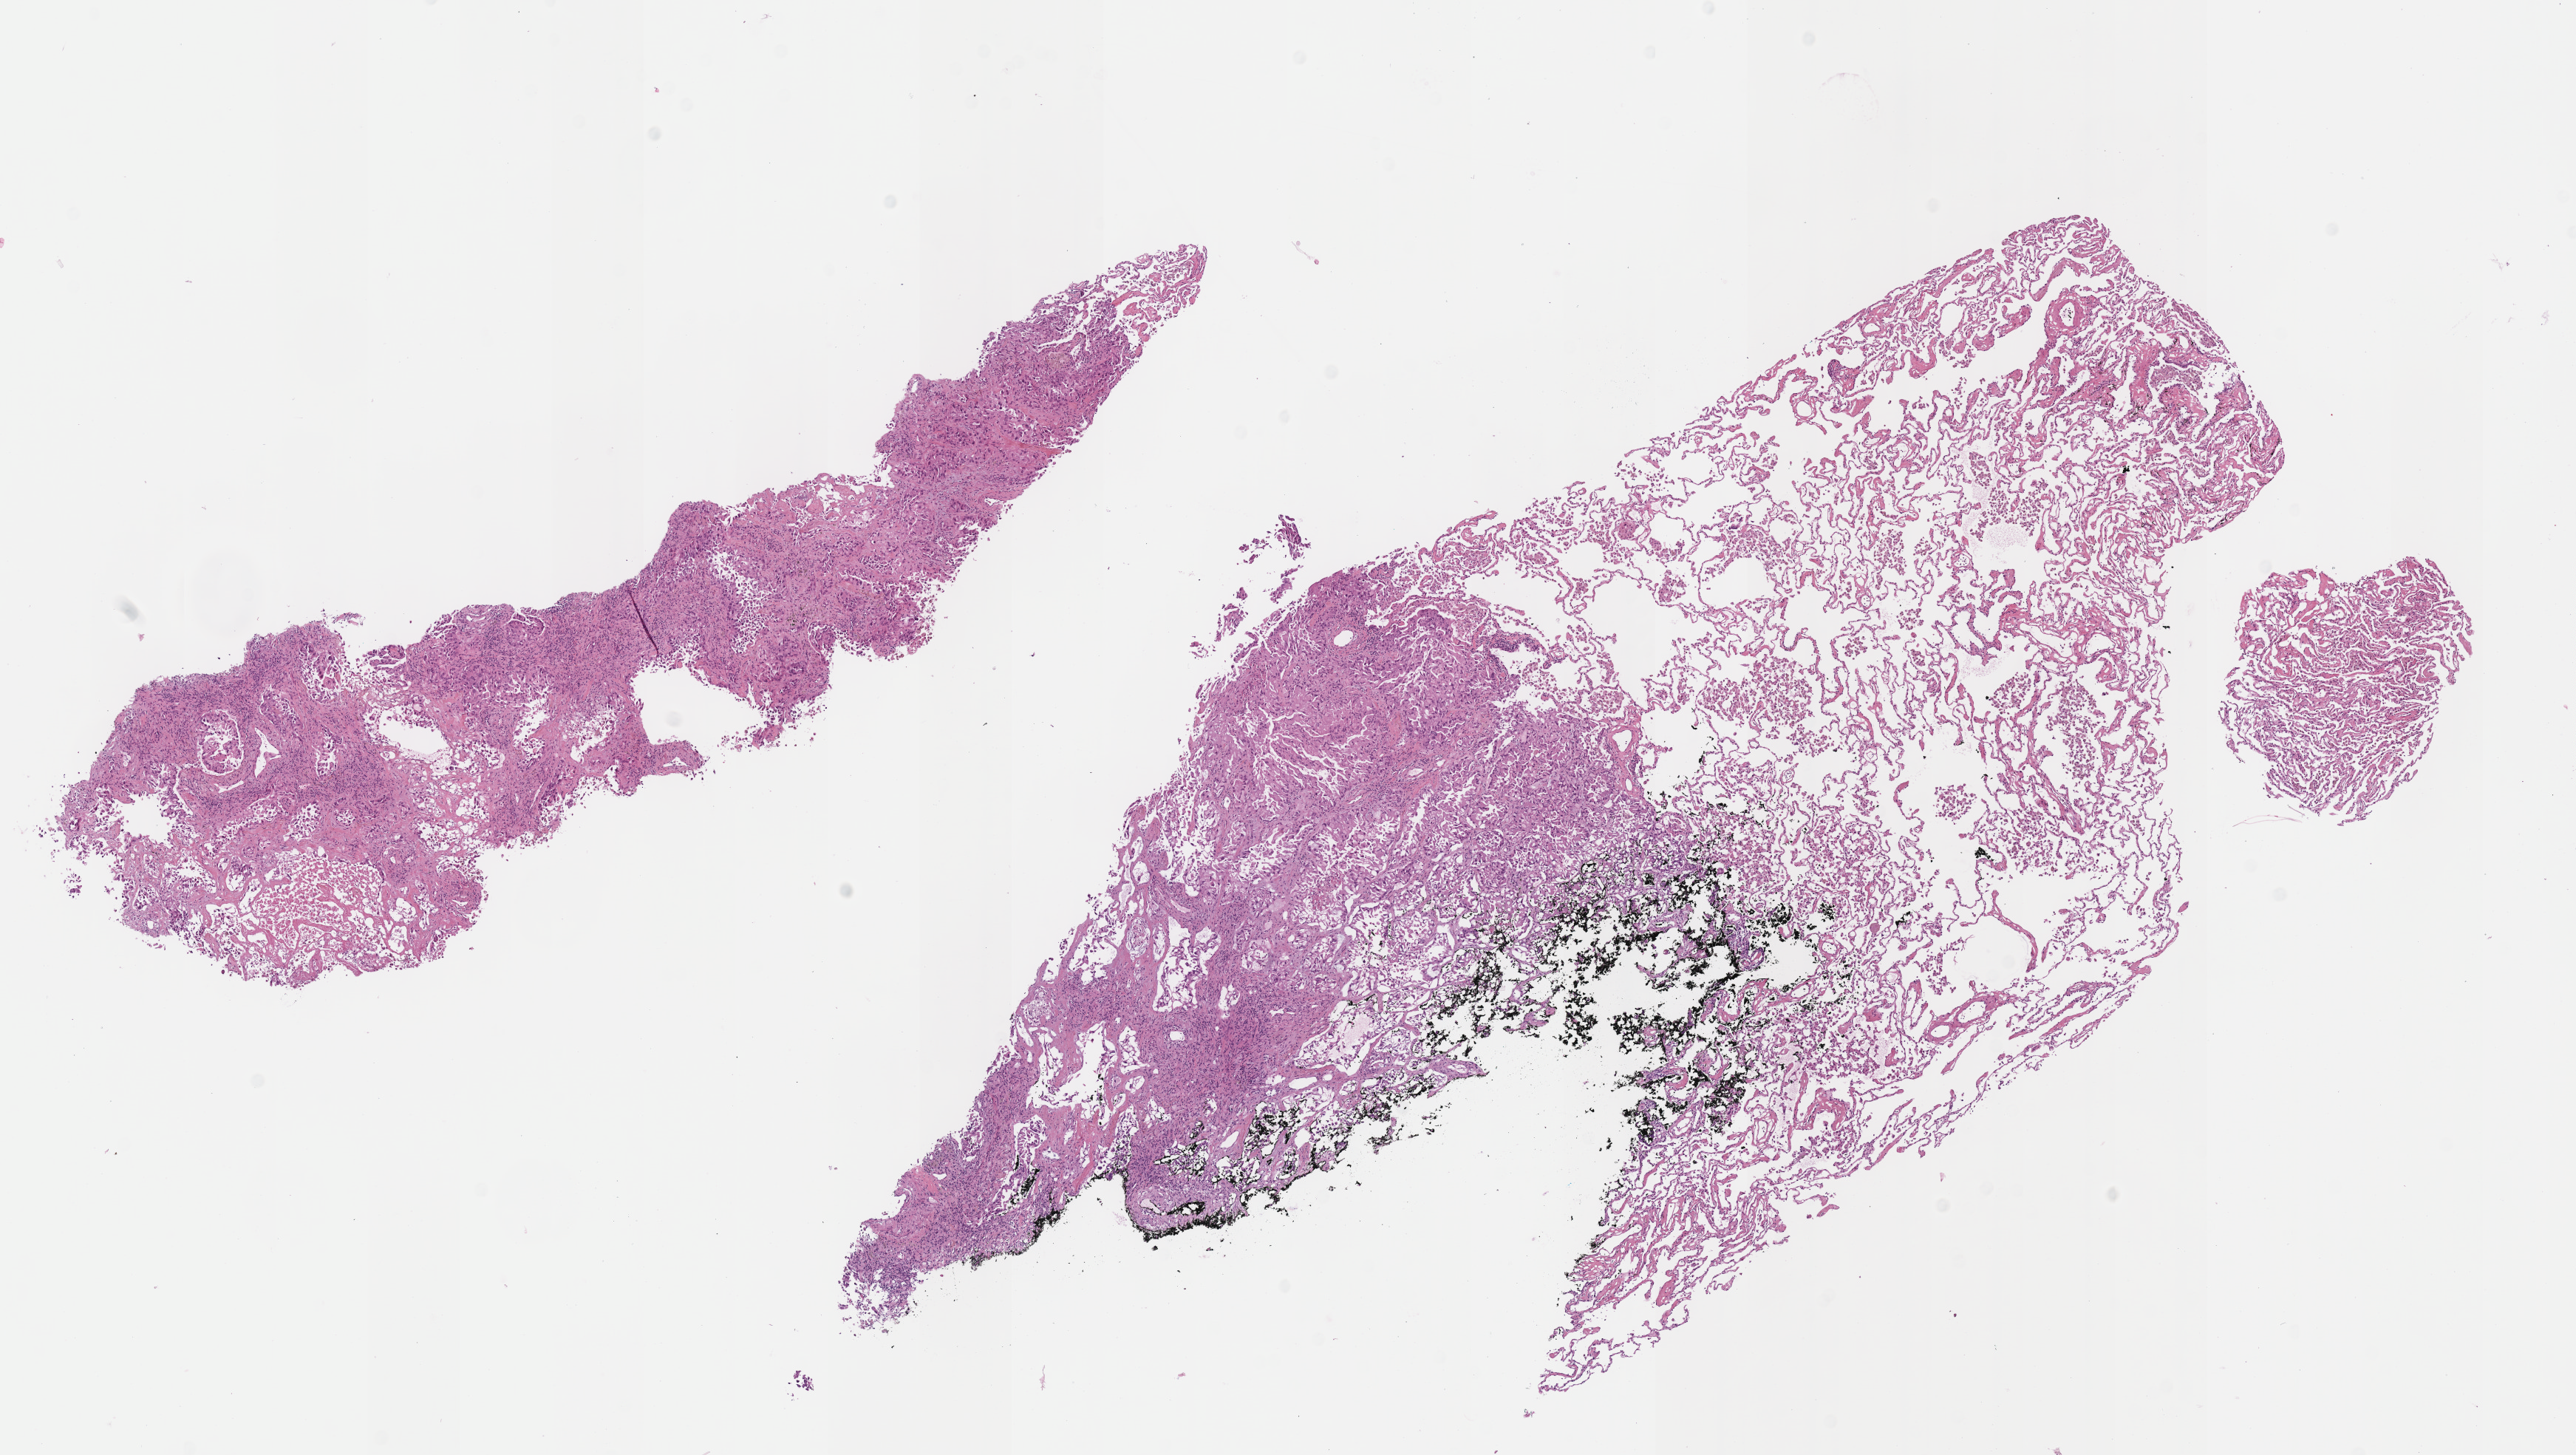
H&E whole-slide image, low-resolution overview of the scanned area, about 13.7 x 7.7 mm, FFPE section, lung, primary tumour sample. Male, age 54 years at initial diagnosis.
Pathologic diagnosis: Adenocarcinoma, NOS (lower lobe, lung).